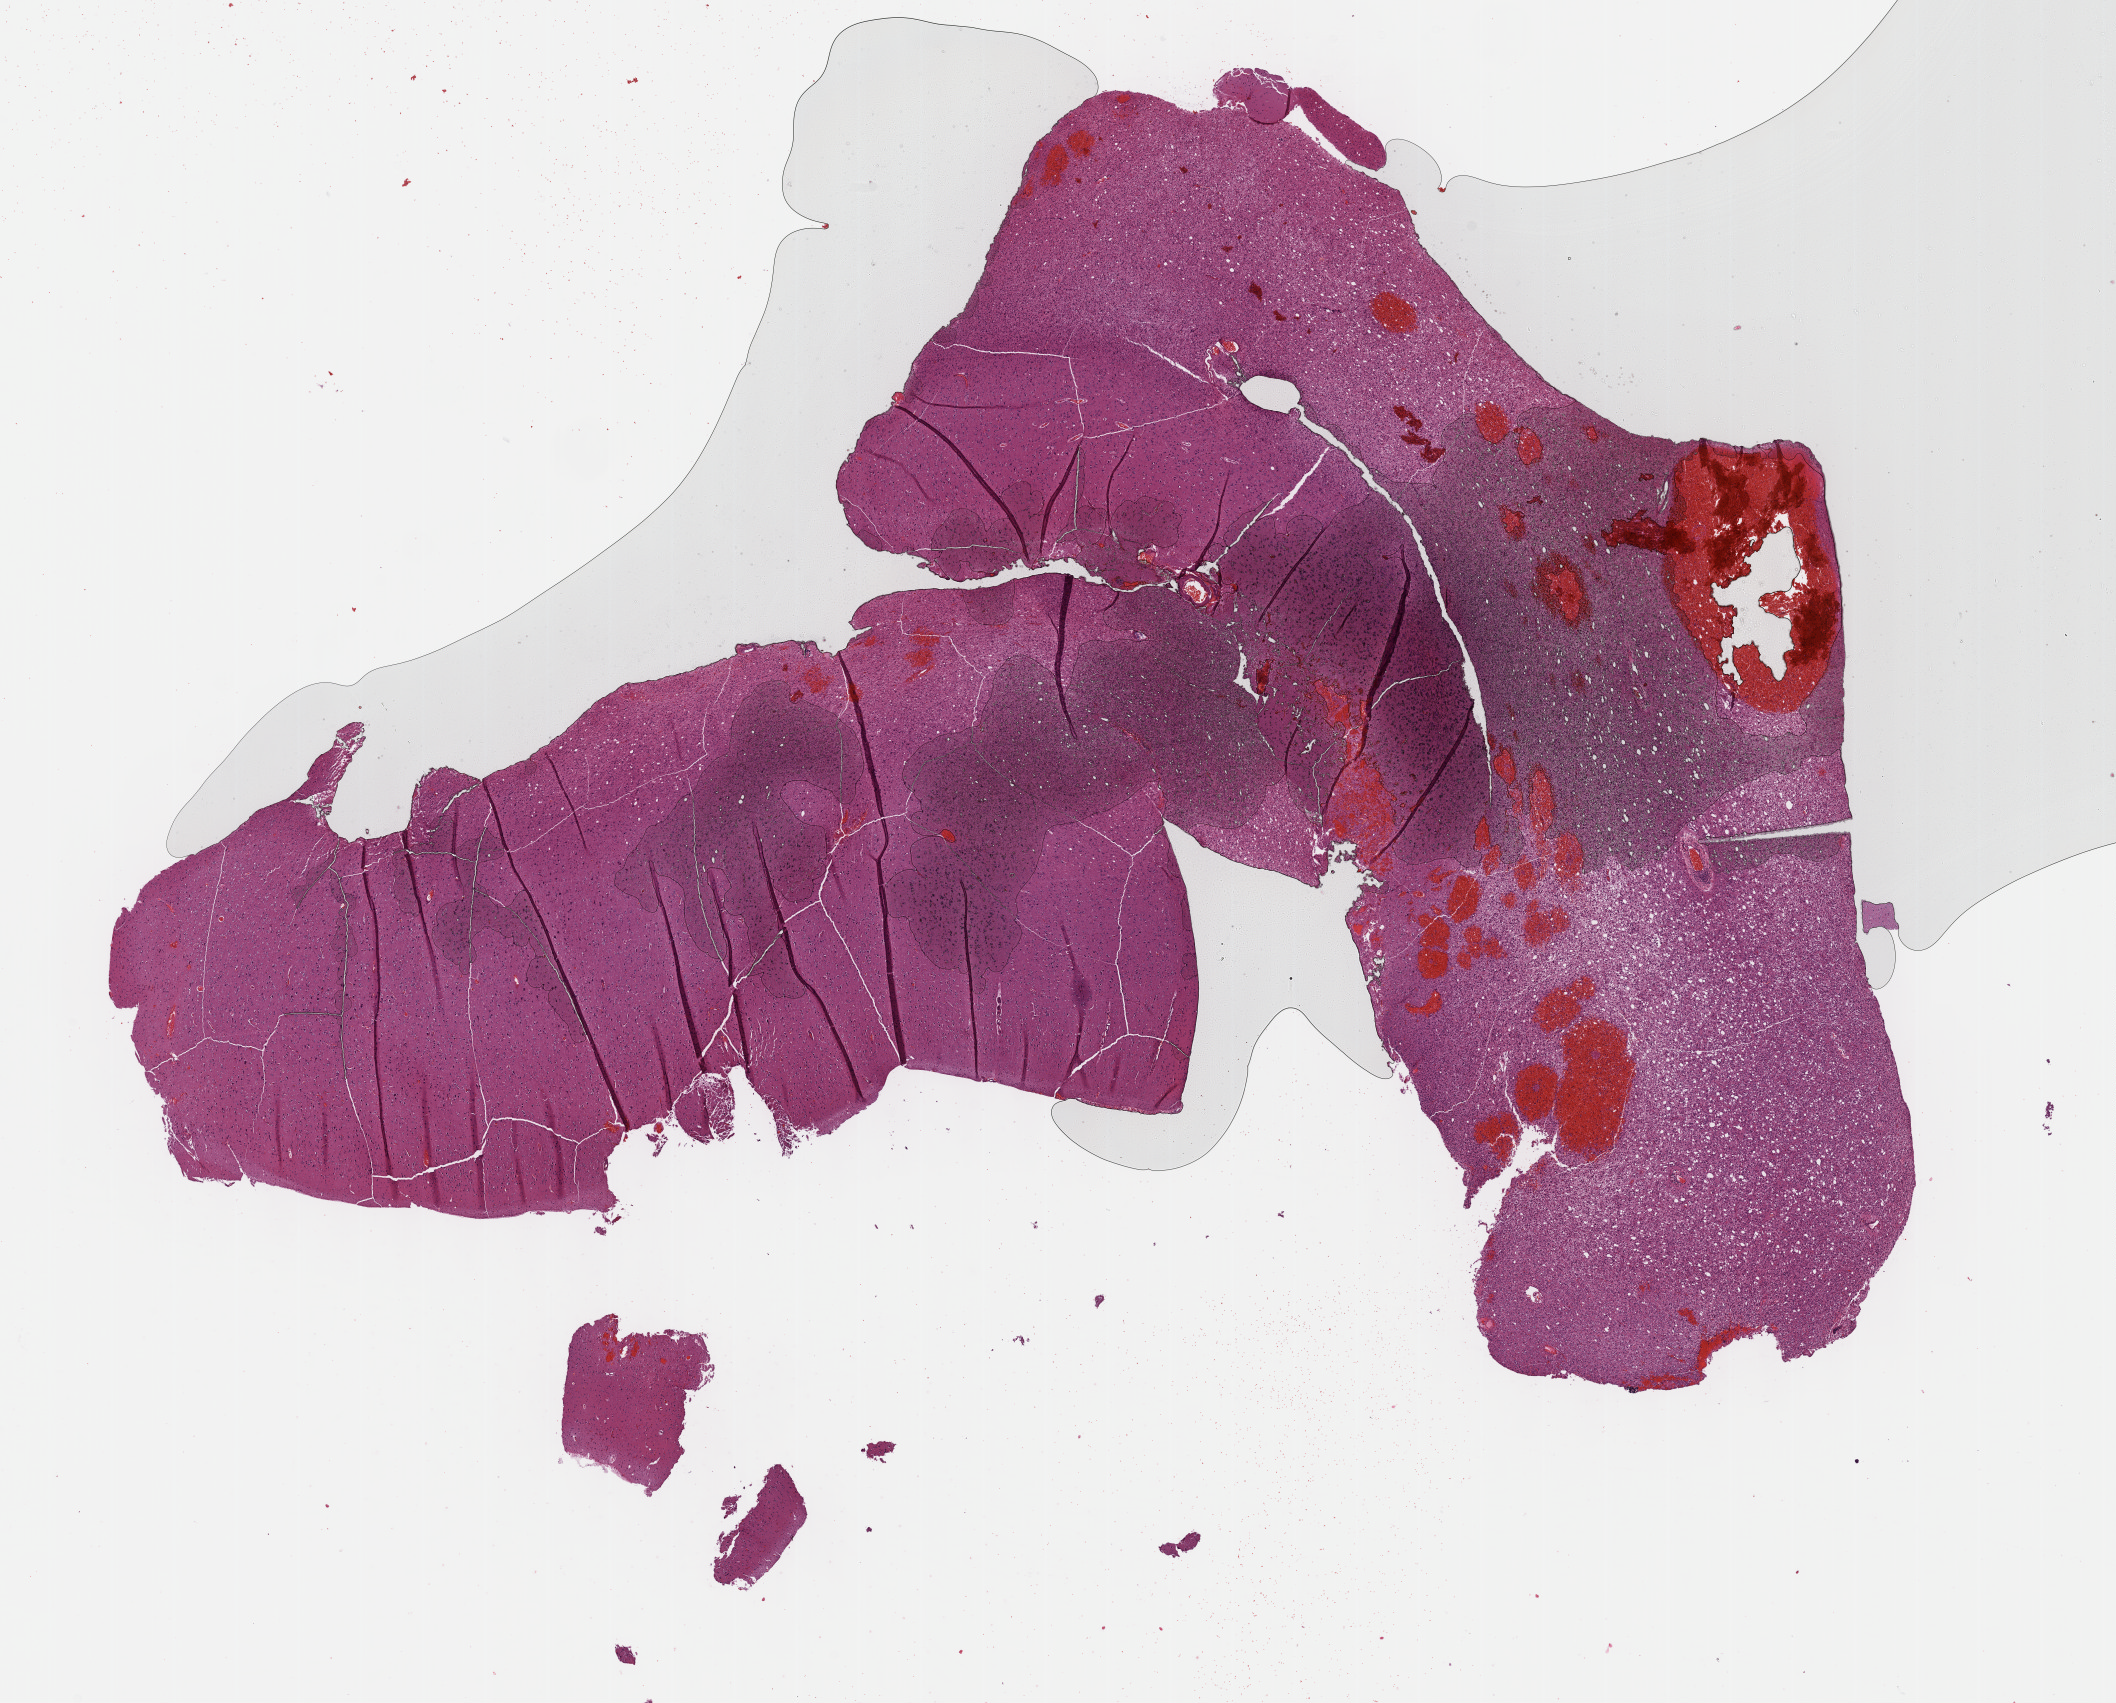
Digitized H&E-stained tissue section (whole slide), whole scanned area (about 17.1 x 13.8 mm, slide scanned at 40x) shown as a low-resolution overview, formalin-fixed paraffin-embedded (FFPE) diagnostic section, sample: primary tumour, brain. Patient: female, age at initial diagnosis 29 years. Histologic grade: G2 (moderately differentiated).
Pathologic diagnosis: Mixed glioma (cerebrum).